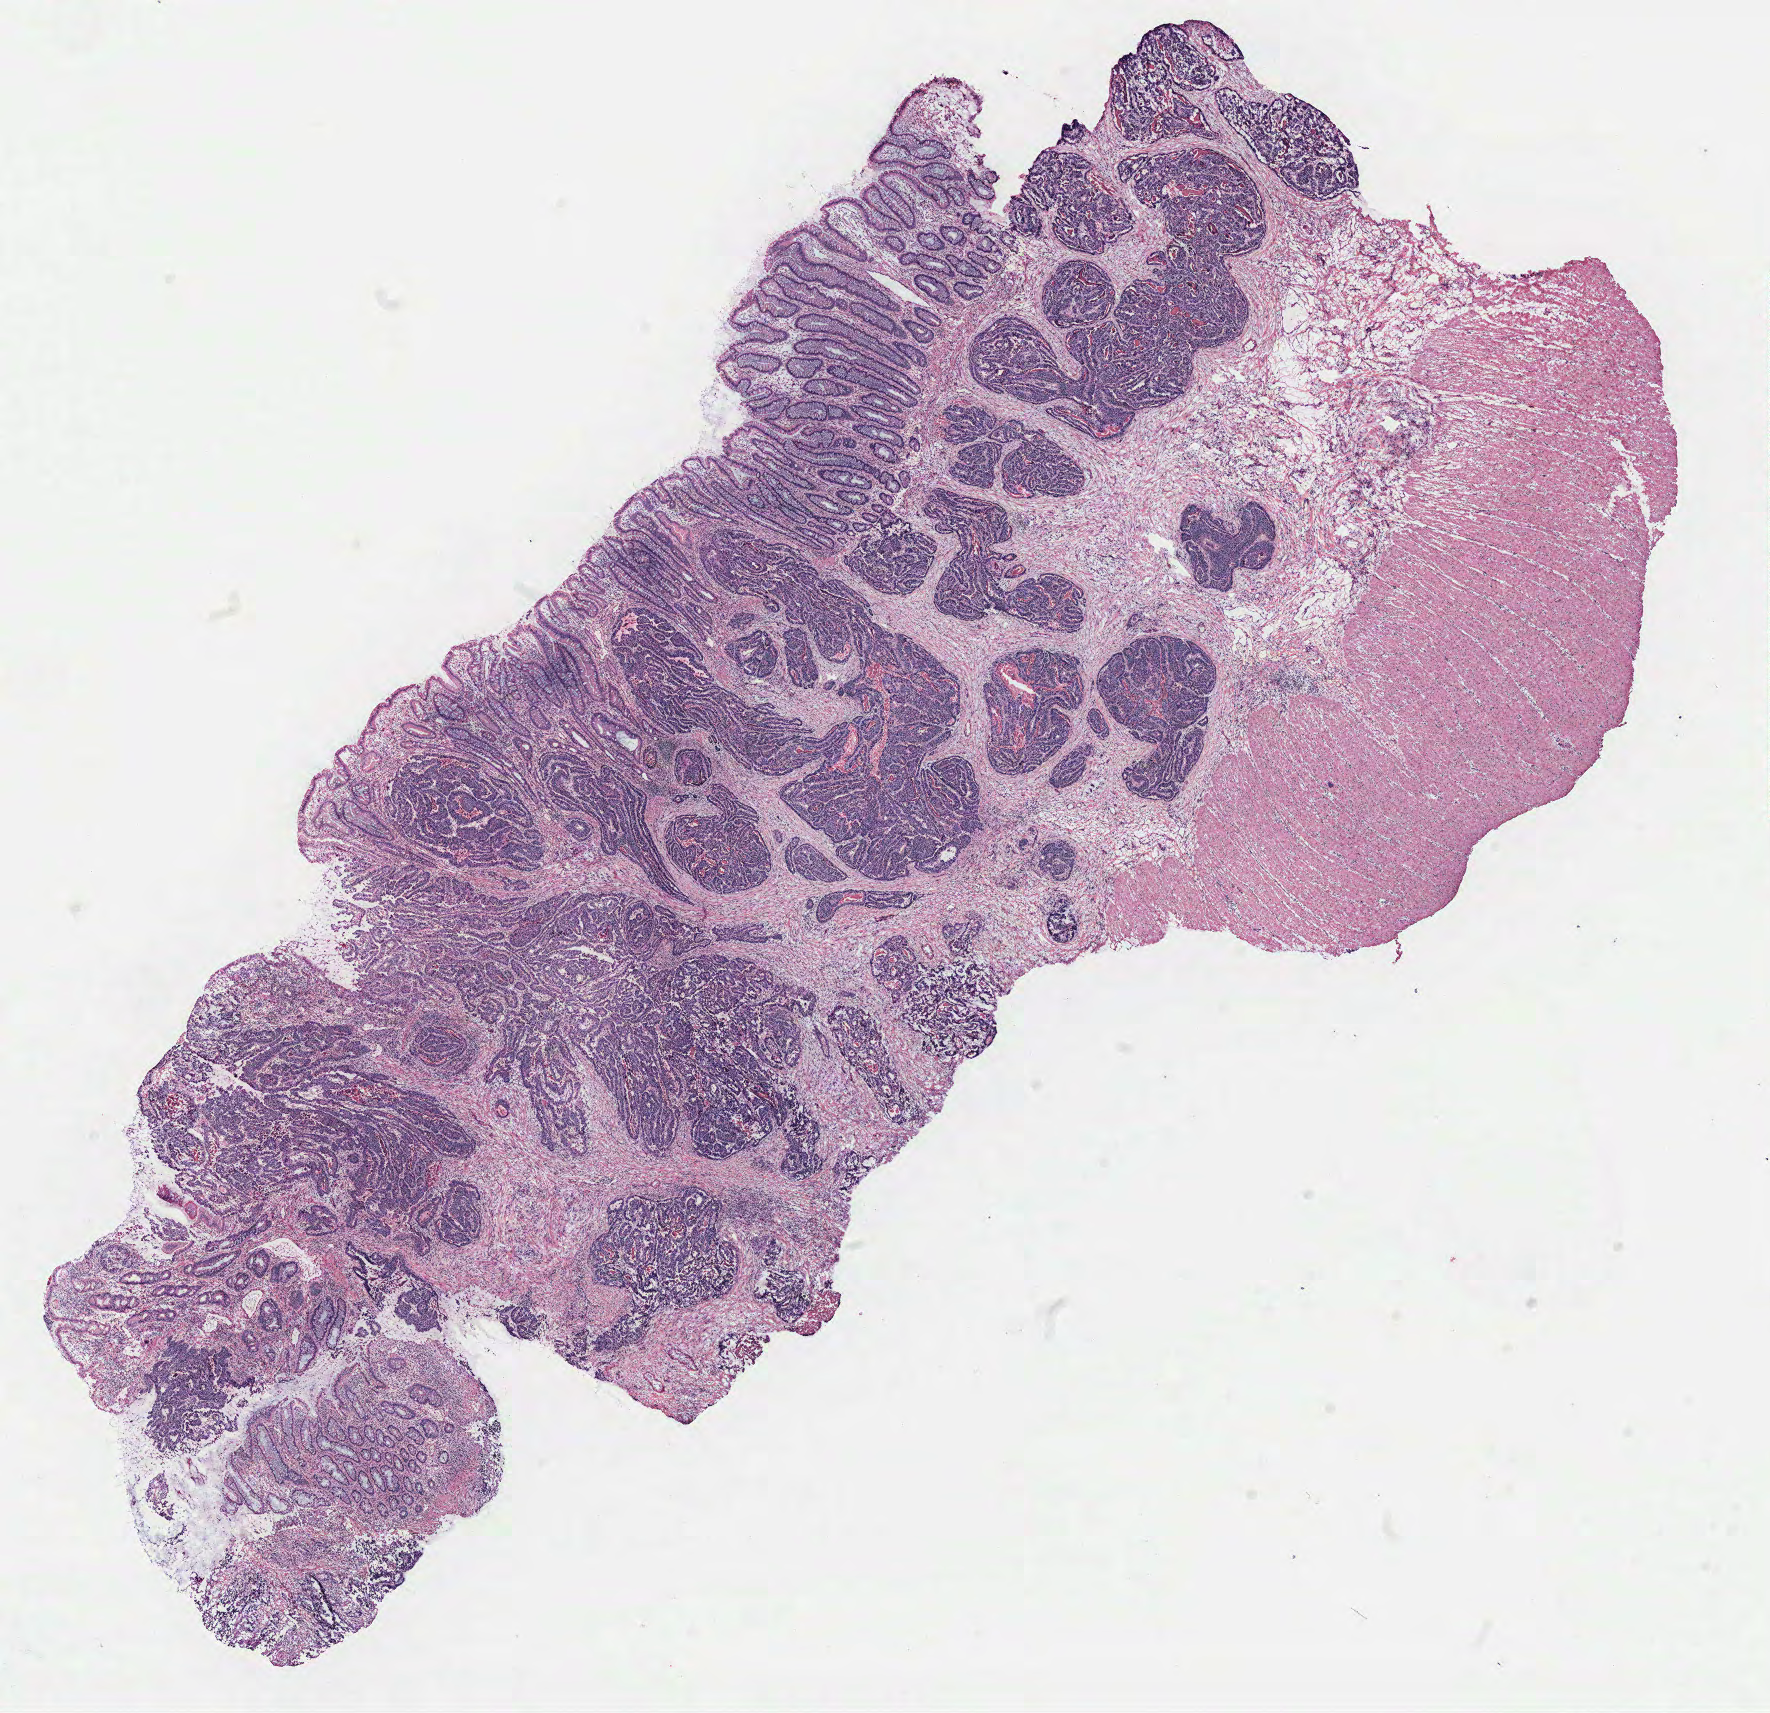
Digitized H&E tissue section (whole slide), low-resolution overview of the scanned area, about 14.2 x 13.7 mm (slide scanned at 40x). Normal (non-tumour) tissue sample, colon. 39-year-old male patient.
• this section: normal (non-tumour) tissue from the same patient
• patient diagnosis: Adenocarcinoma, NOS